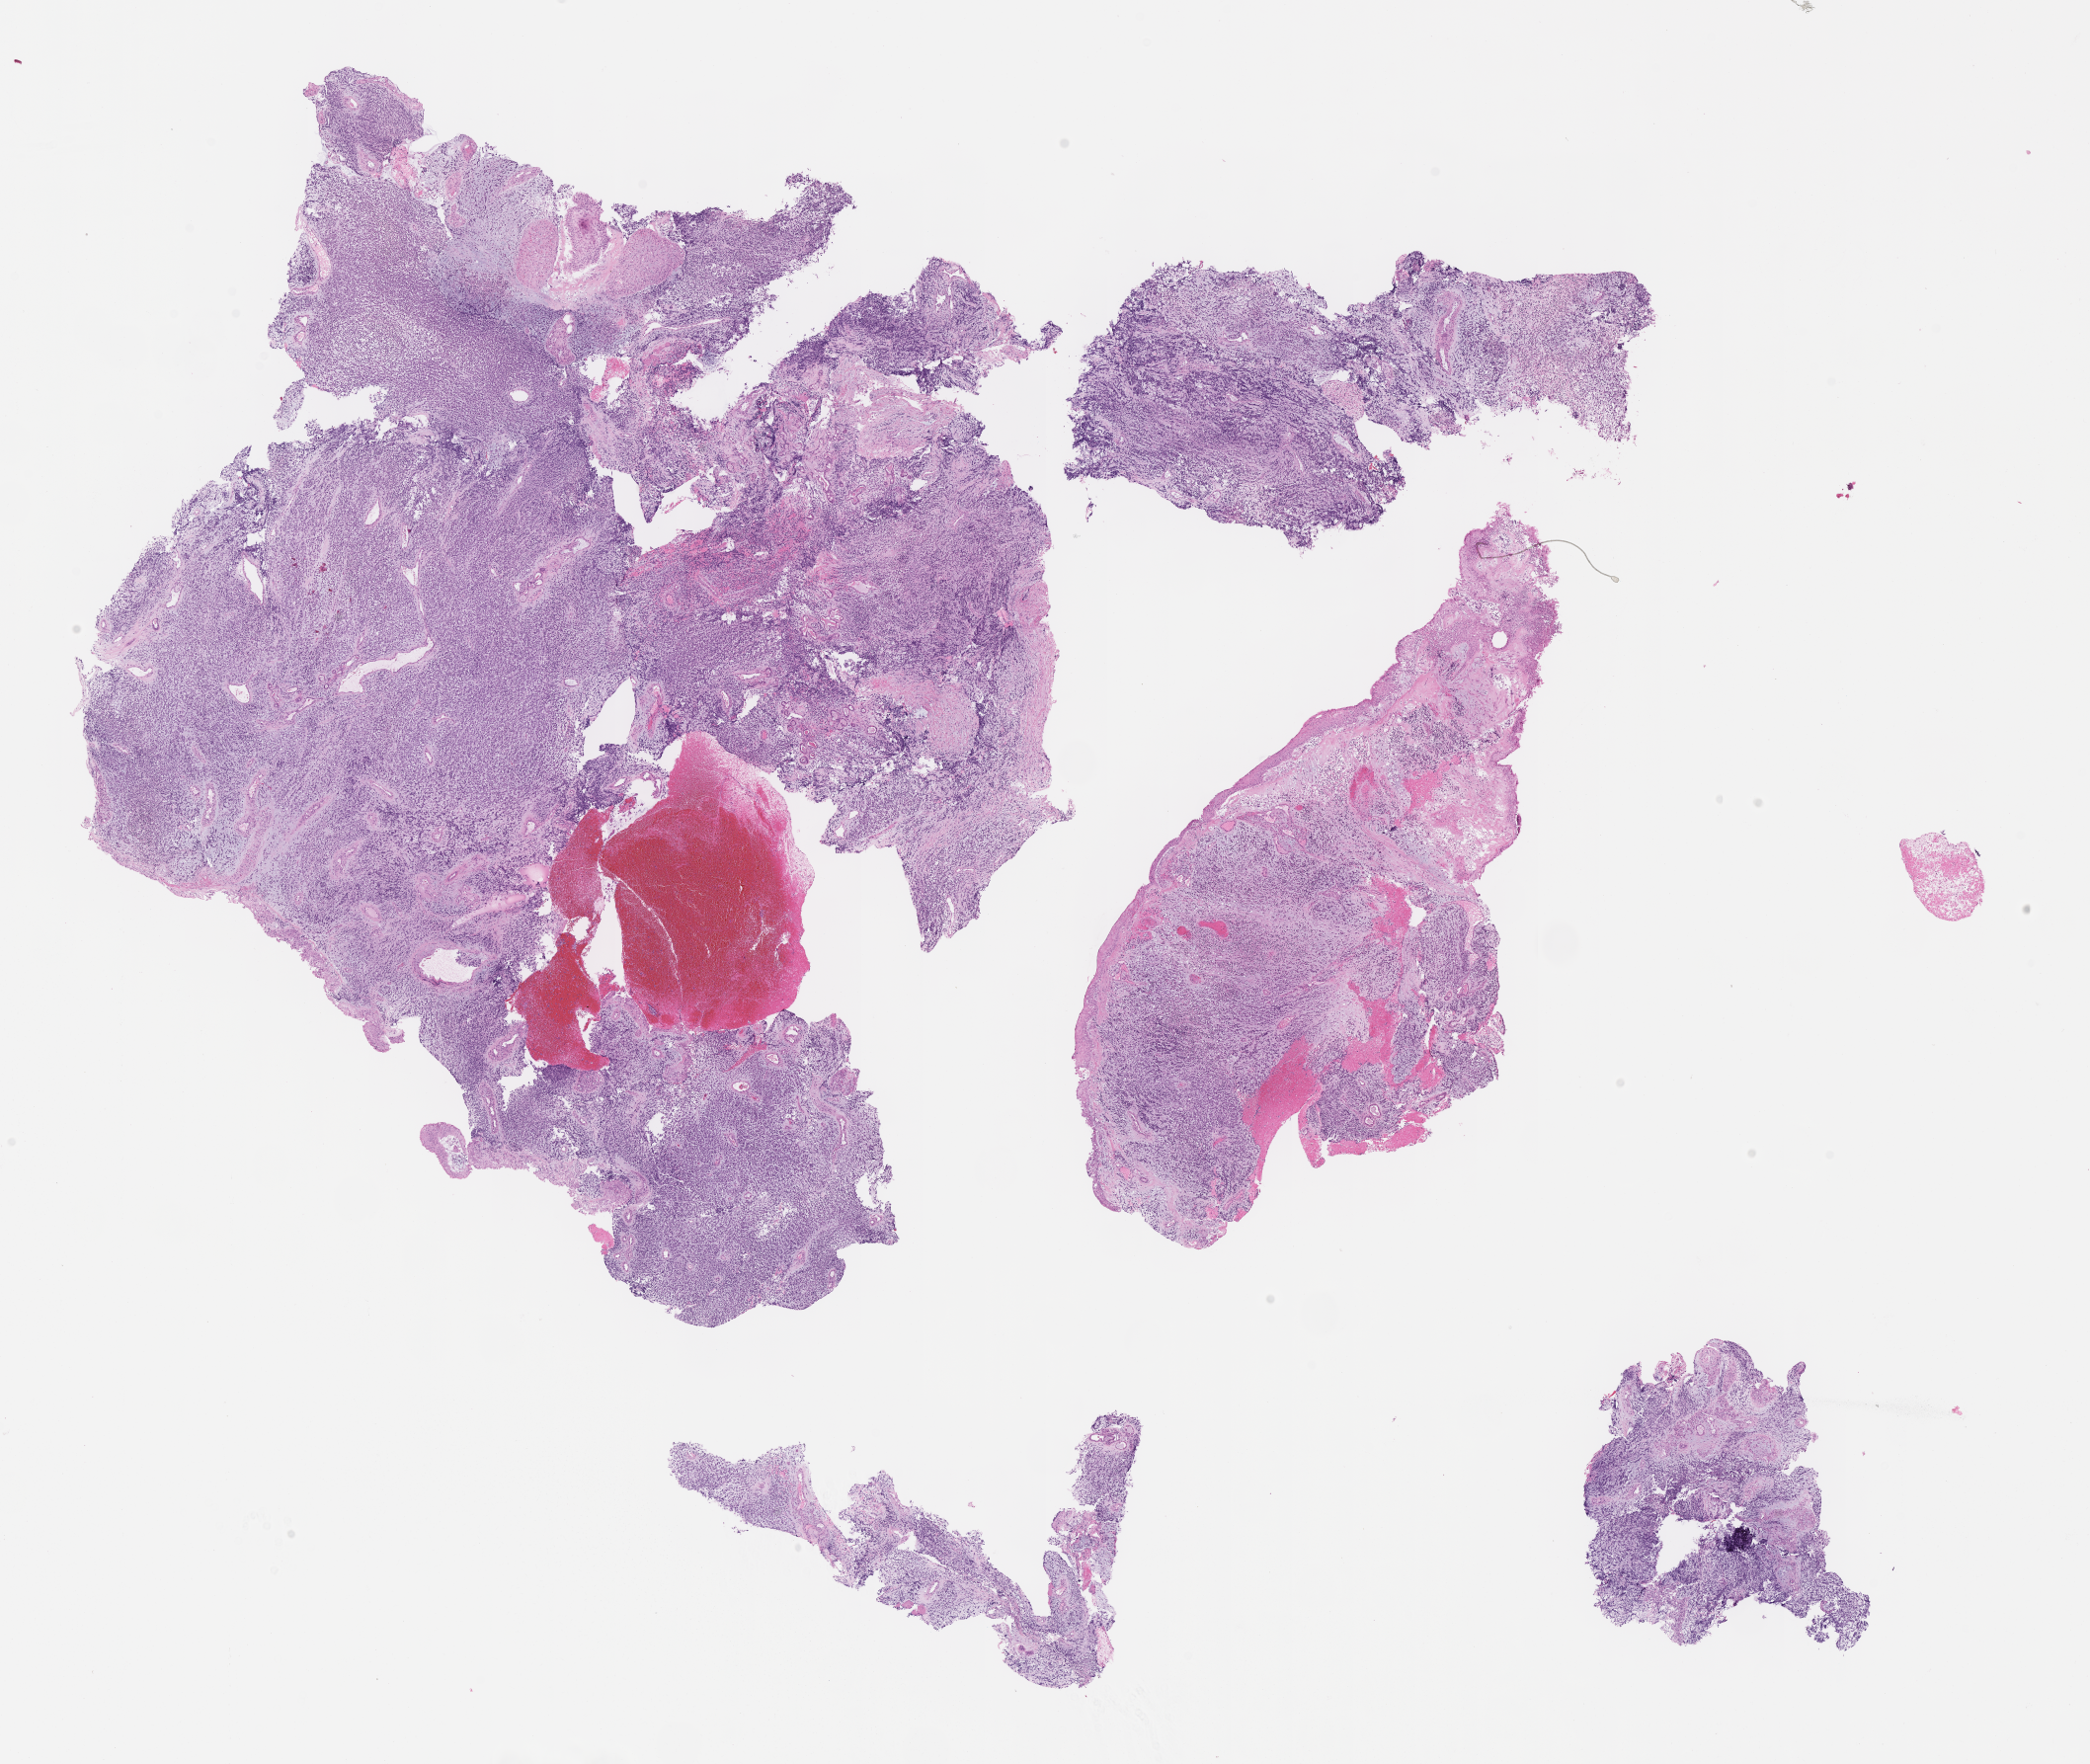
Digitized hematoxylin and eosin (H&E)-stained section of tumor tissue — a low-resolution overview of the entire scanned area, about 17.1 x 14.4 mm, formalin-fixed paraffin-embedded section, sample anatomic site: nasopharynx. Male patient, age at diagnosis 11.3 years.
Diagnosis: rhabdomyosarcoma; histological classification: embryonal rhabdomyosarcoma. Metastatic status at presentation (as recorded): non-metastatic. Stage (as recorded): 1.